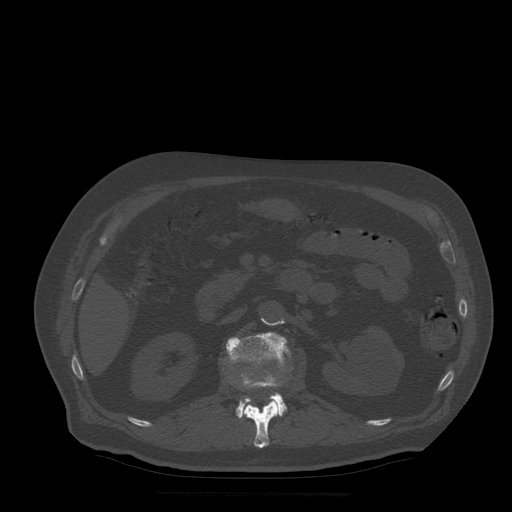
CT including the spine, one axial slice; slice 184 of 522 in the series (ordered by position); bone window (W 1800 / L 400 HU); 512 × 512 image matrix, field of view 420 × 420 mm. Patient age 72 years. From the clinical record (not read from this slice): primary cancer: prostate.
Annotated regions visible in this slice (semi-automatically segmented with operator editing):
- L1 vertebra: box from (x=240, y=374) to (x=282, y=449) px
- L2 vertebra: (x=226, y=332)–(x=289, y=419)